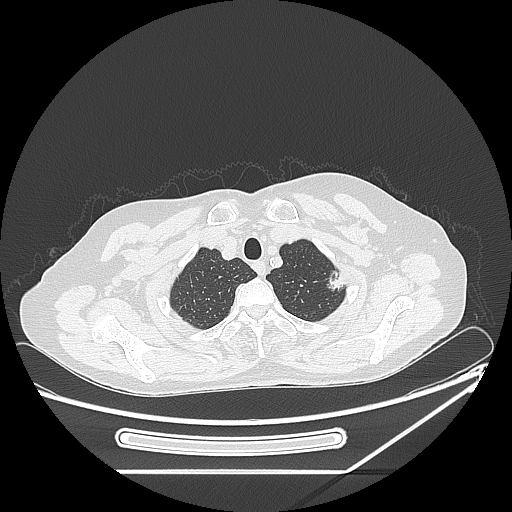
Chest CT, one axial slice. Position 213 of 250 along the scan axis. Lung window (W 1500 / L -600 HU). 1.25 mm slice thickness. 512 × 512 image matrix. Patient: female, 57 years. From the clinical record (not read from this slice): clinical TNM (as recorded): T1c N0 M0; histopathological grade: G2-3.
Outlined on this slice (rectangle marked by the reading radiologist):
- lung tumour (recorded histology: adenocarcinoma): bounding box [x1, y1, x2, y2] px = [323, 265, 349, 295]